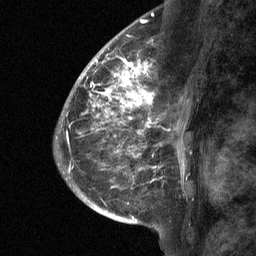
Breast MRI (dynamic contrast-enhanced), one sagittal slice. Slice 38 of 64 in the series (ordered by position). Dynamic contrast-enhanced study with each time point stored as its own series, time point 2 of 3 at this slice position (early post-contrast, ordered by acquisition time). 1.5 T. TE 4.8 ms, TR 27 ms. 2 mm slice thickness. 256 × 256 image matrix, field of view 180 × 180 mm. Patient: female, 59 years. Case-level facts recorded for this patient, not image findings: setting: breast cancer imaged before/during neoadjuvant chemotherapy; receptor status: triple-negative.
Annotated regions visible in this slice (semi-automatically segmented with operator editing):
- analysis volume of interest (the breast-tissue region the enhancement analysis was run in; not a lesion): box from (x=122, y=58) to (x=172, y=109) px
- tumour enhancement mask (voxels above the 90 % enhancement threshold inside the analysis volume of interest): (x=122, y=58)–(x=155, y=109)